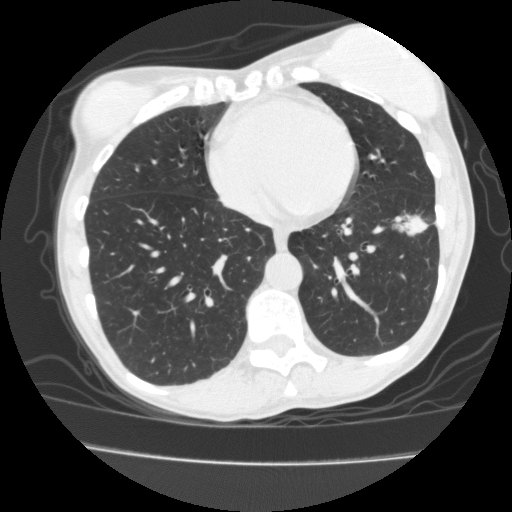
Low-dose screening chest CT, one axial slice; position 61 of 171 along the scan axis; reconstruction kernel FC10; lung window (W 1500 / L -600 HU); 2 mm slice thickness; 512 × 512 image matrix.
Annotated regions visible in this slice (expert manual segmentation):
- lesion 1 (tumor, lower lobe of left lung): bounding box <404,216,427,234> (left, top, right, bottom; pixels)